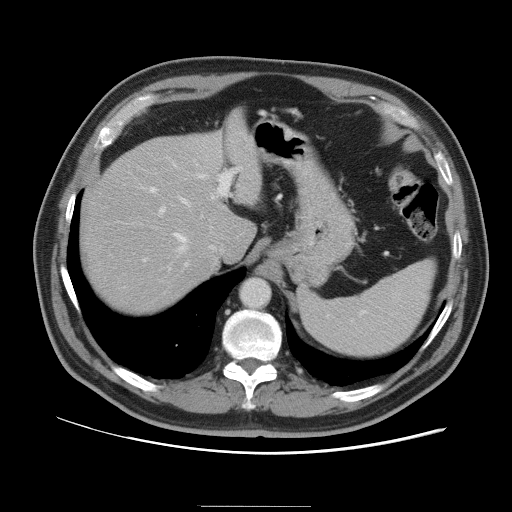
Contrast-enhanced abdominal CT, one axial slice. Position 75 of 105 along the scan axis. 120 kVp. Intravenous contrast given. Soft-tissue window (W 400 / L 40 HU). 5 mm slice thickness. 512 × 512 image matrix. Male patient, age 64 years. Case-level facts recorded for this patient, not image findings: diagnosis: colorectal cancer liver metastases, imaged before liver resection.
Outlined on this slice (outlined manually by an expert reader):
- hepatic veins: bounding box (x1, y1, x2, y2) in pixels: (174, 196, 190, 252)
- liver: (81, 114, 262, 313)
- planned liver remnant (the part of the liver to remain after resection): (81, 145, 245, 314)
- portal vein (with intrahepatic branches): (149, 161, 232, 266)